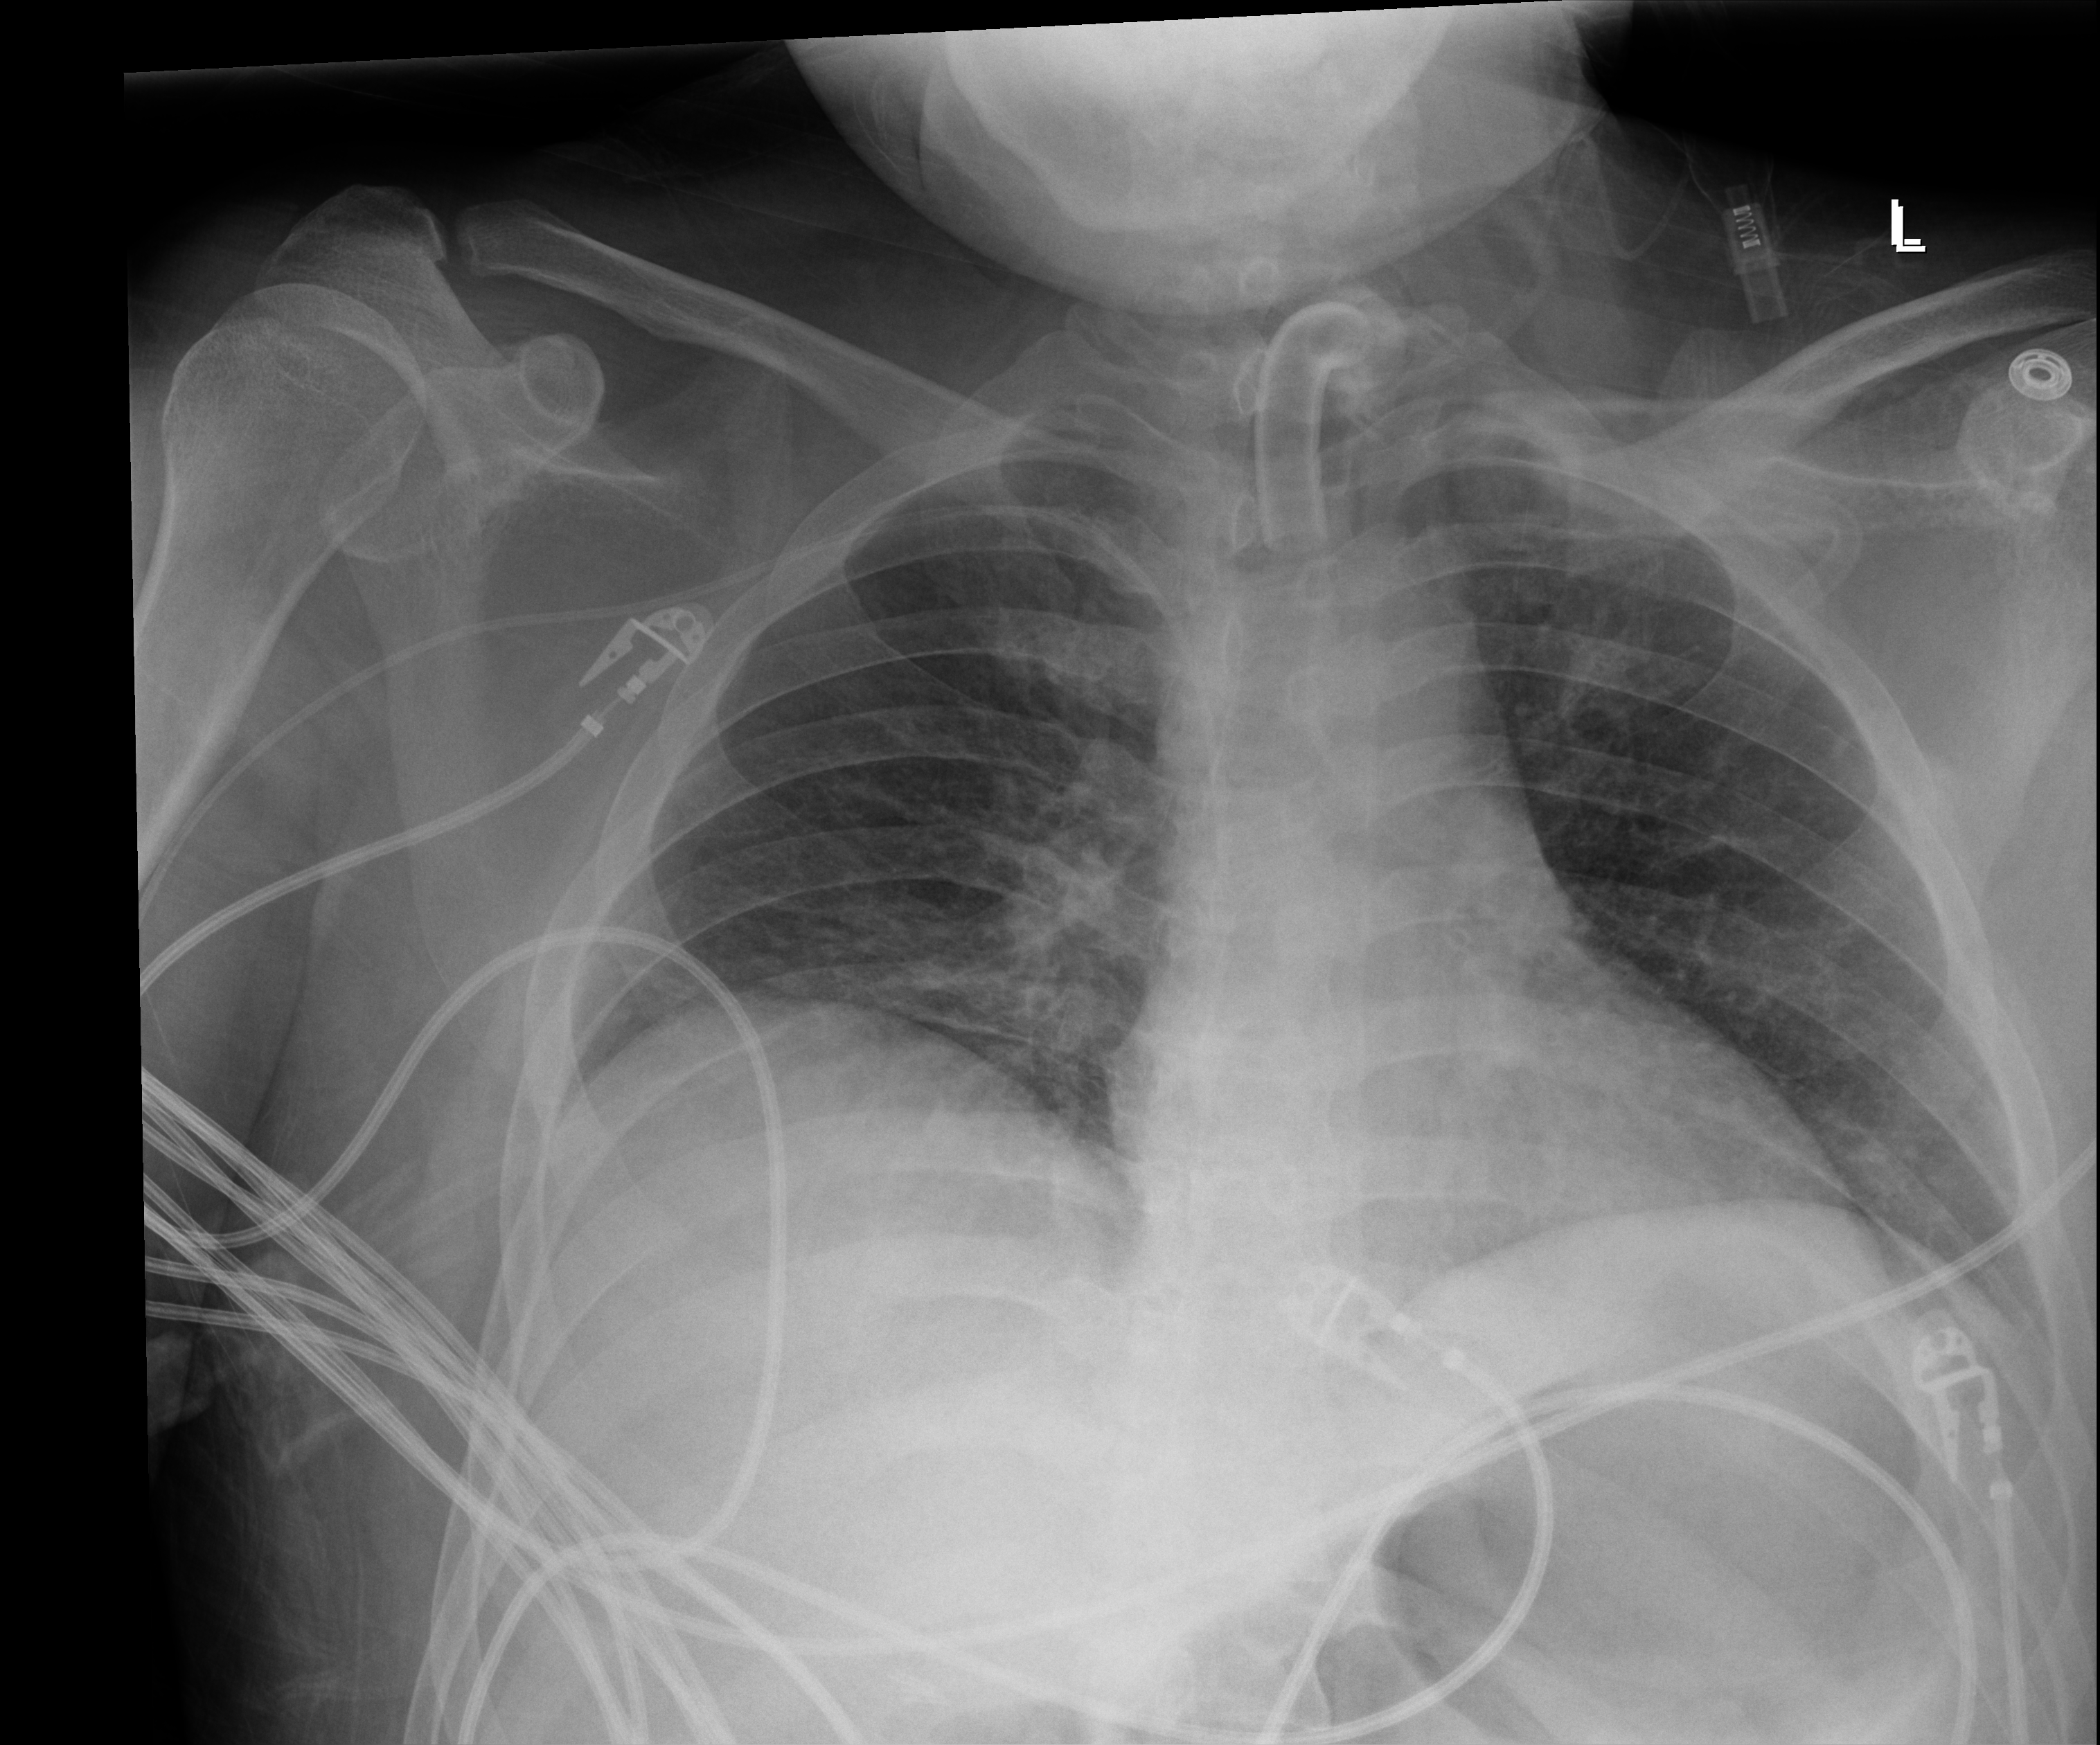
Portable chest radiograph, anteroposterior (AP) projection. Patient hospitalised with COVID-19; male, aged 18–59 years.
Hospital-stay facts (about this admission, not read from this image; timing relative to this image not recorded):
- length of hospital stay: 44 days